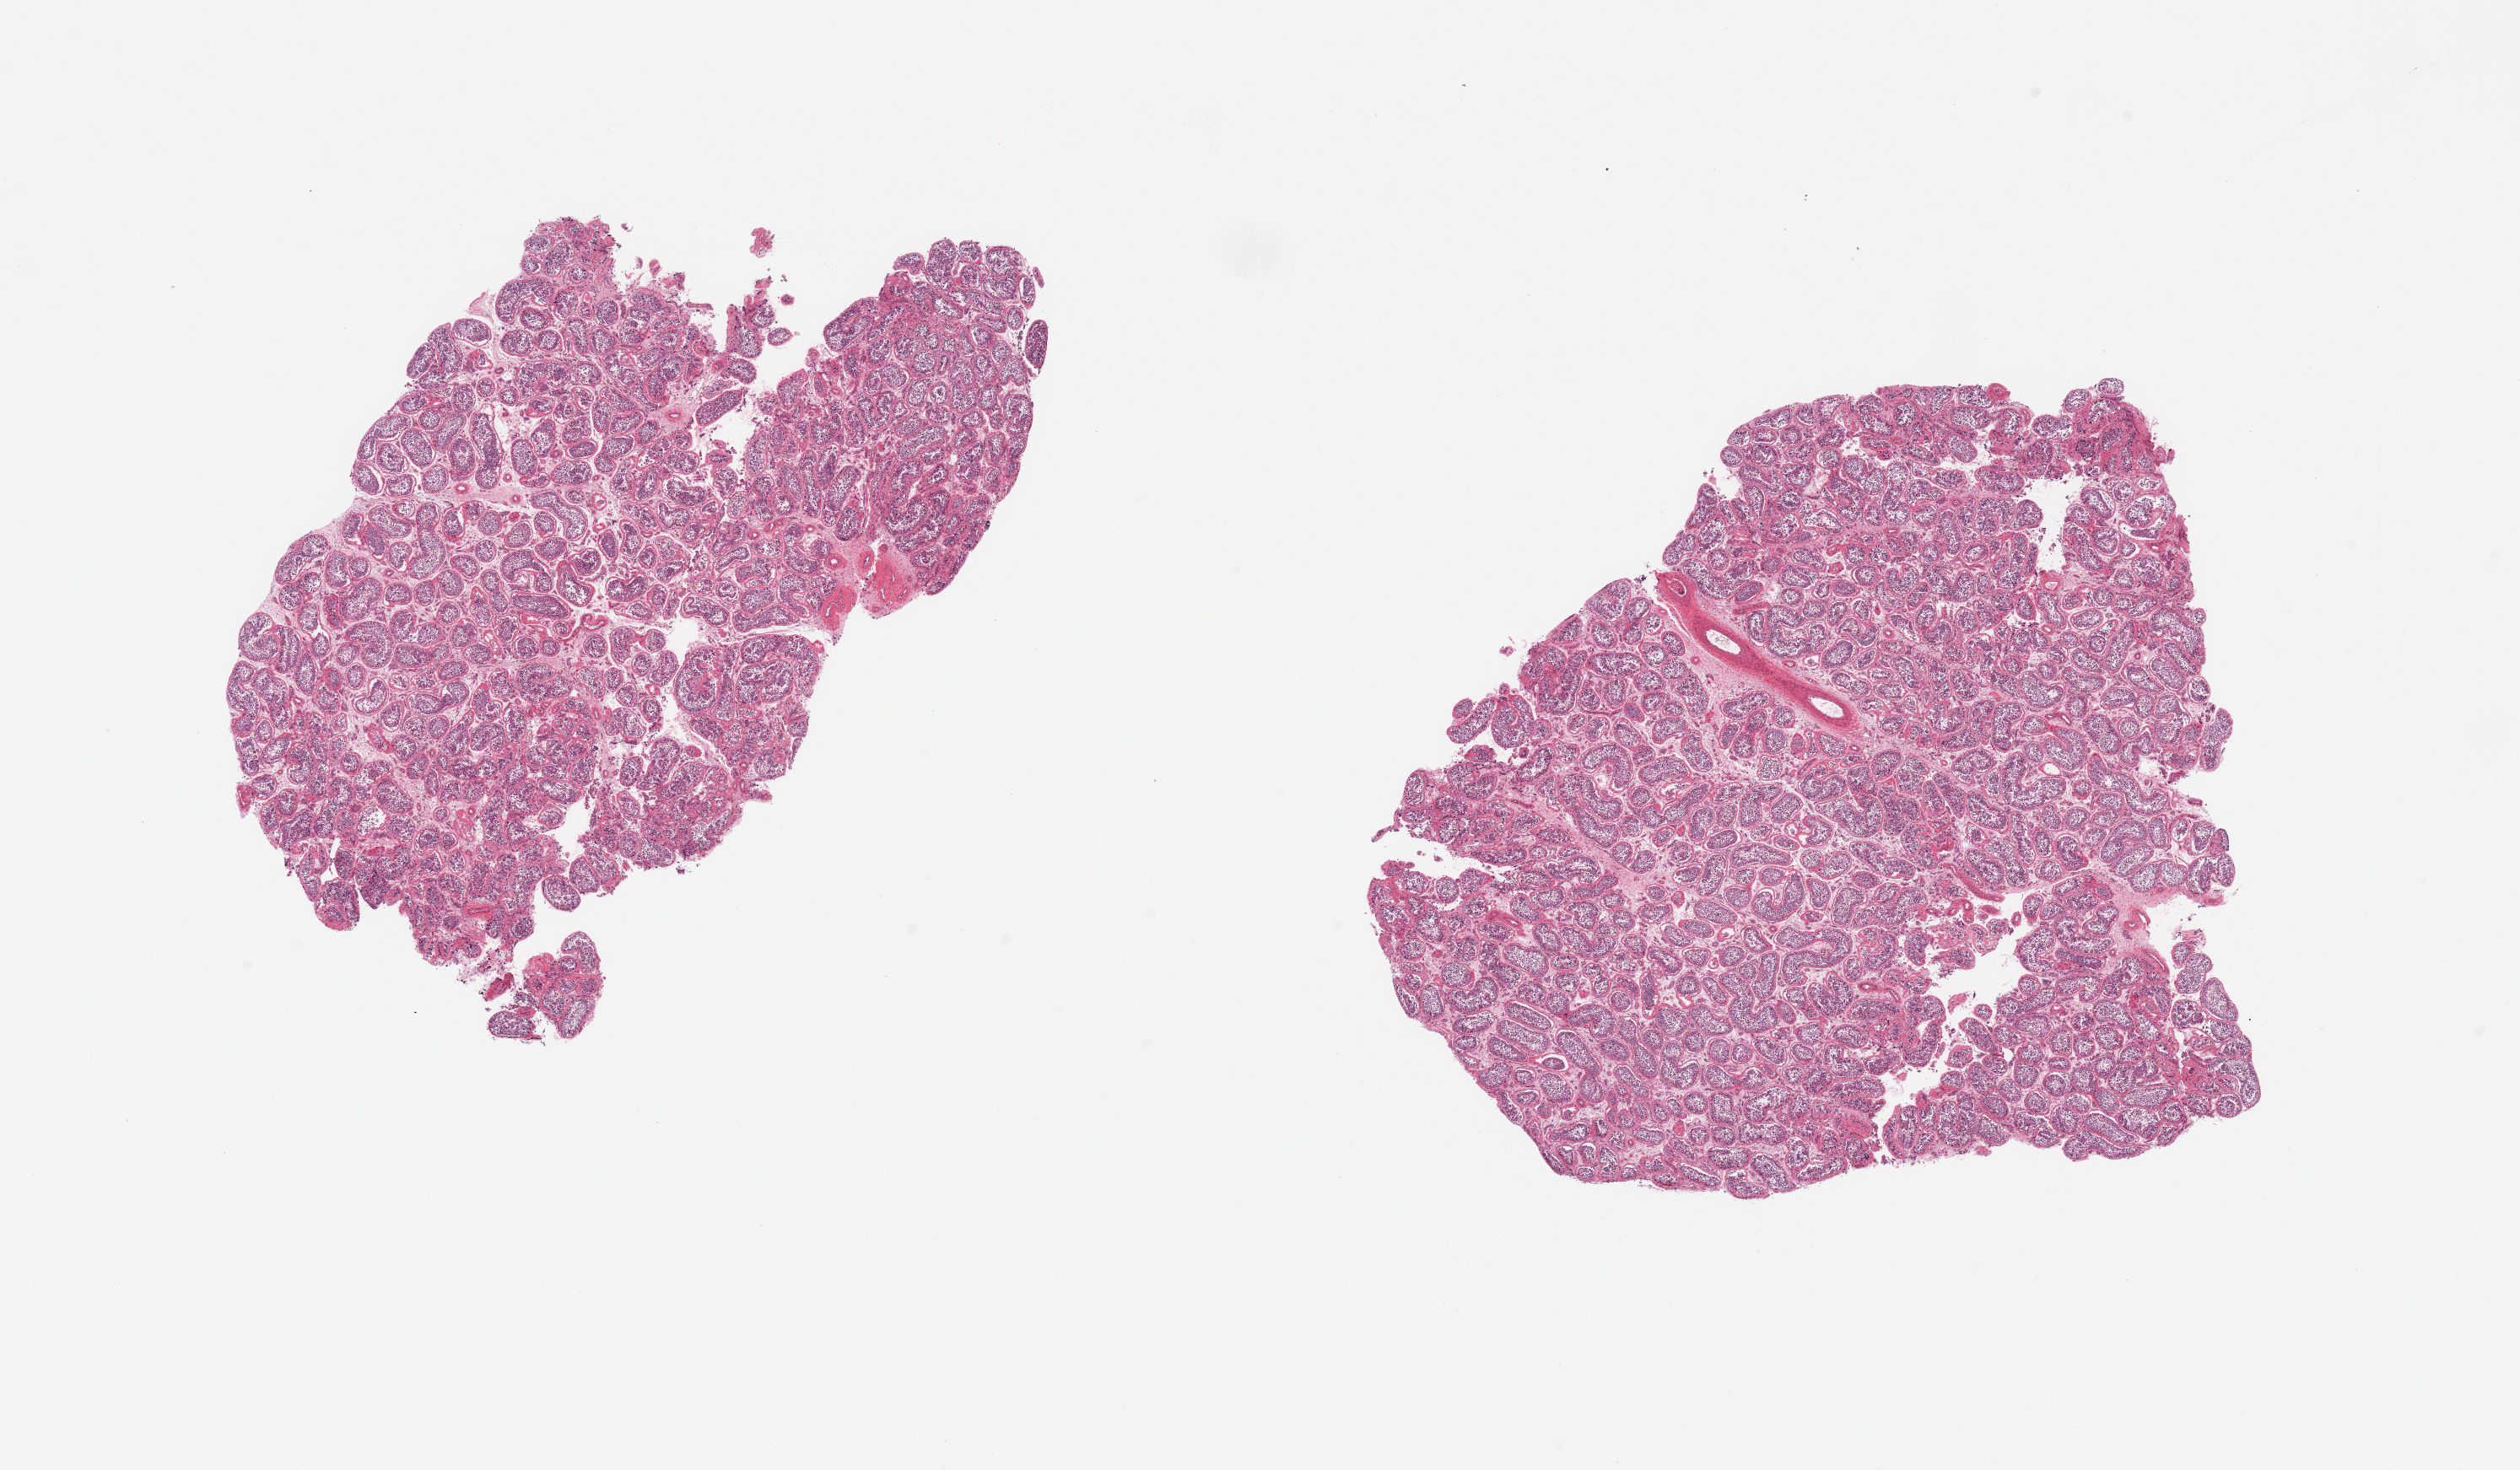
Hematoxylin and eosin (H&E) whole-slide image — a low-resolution overview of the entire scanned area, about 23.6 x 13.8 mm (slide scanned at 20x); PAXgene-fixed, paraffin-embedded tissue; target tissue: testis; tissue donor sample. Donor sex: male.
- reviewer comment on this tissue sample: 2 pieces; spermatogenesis is active